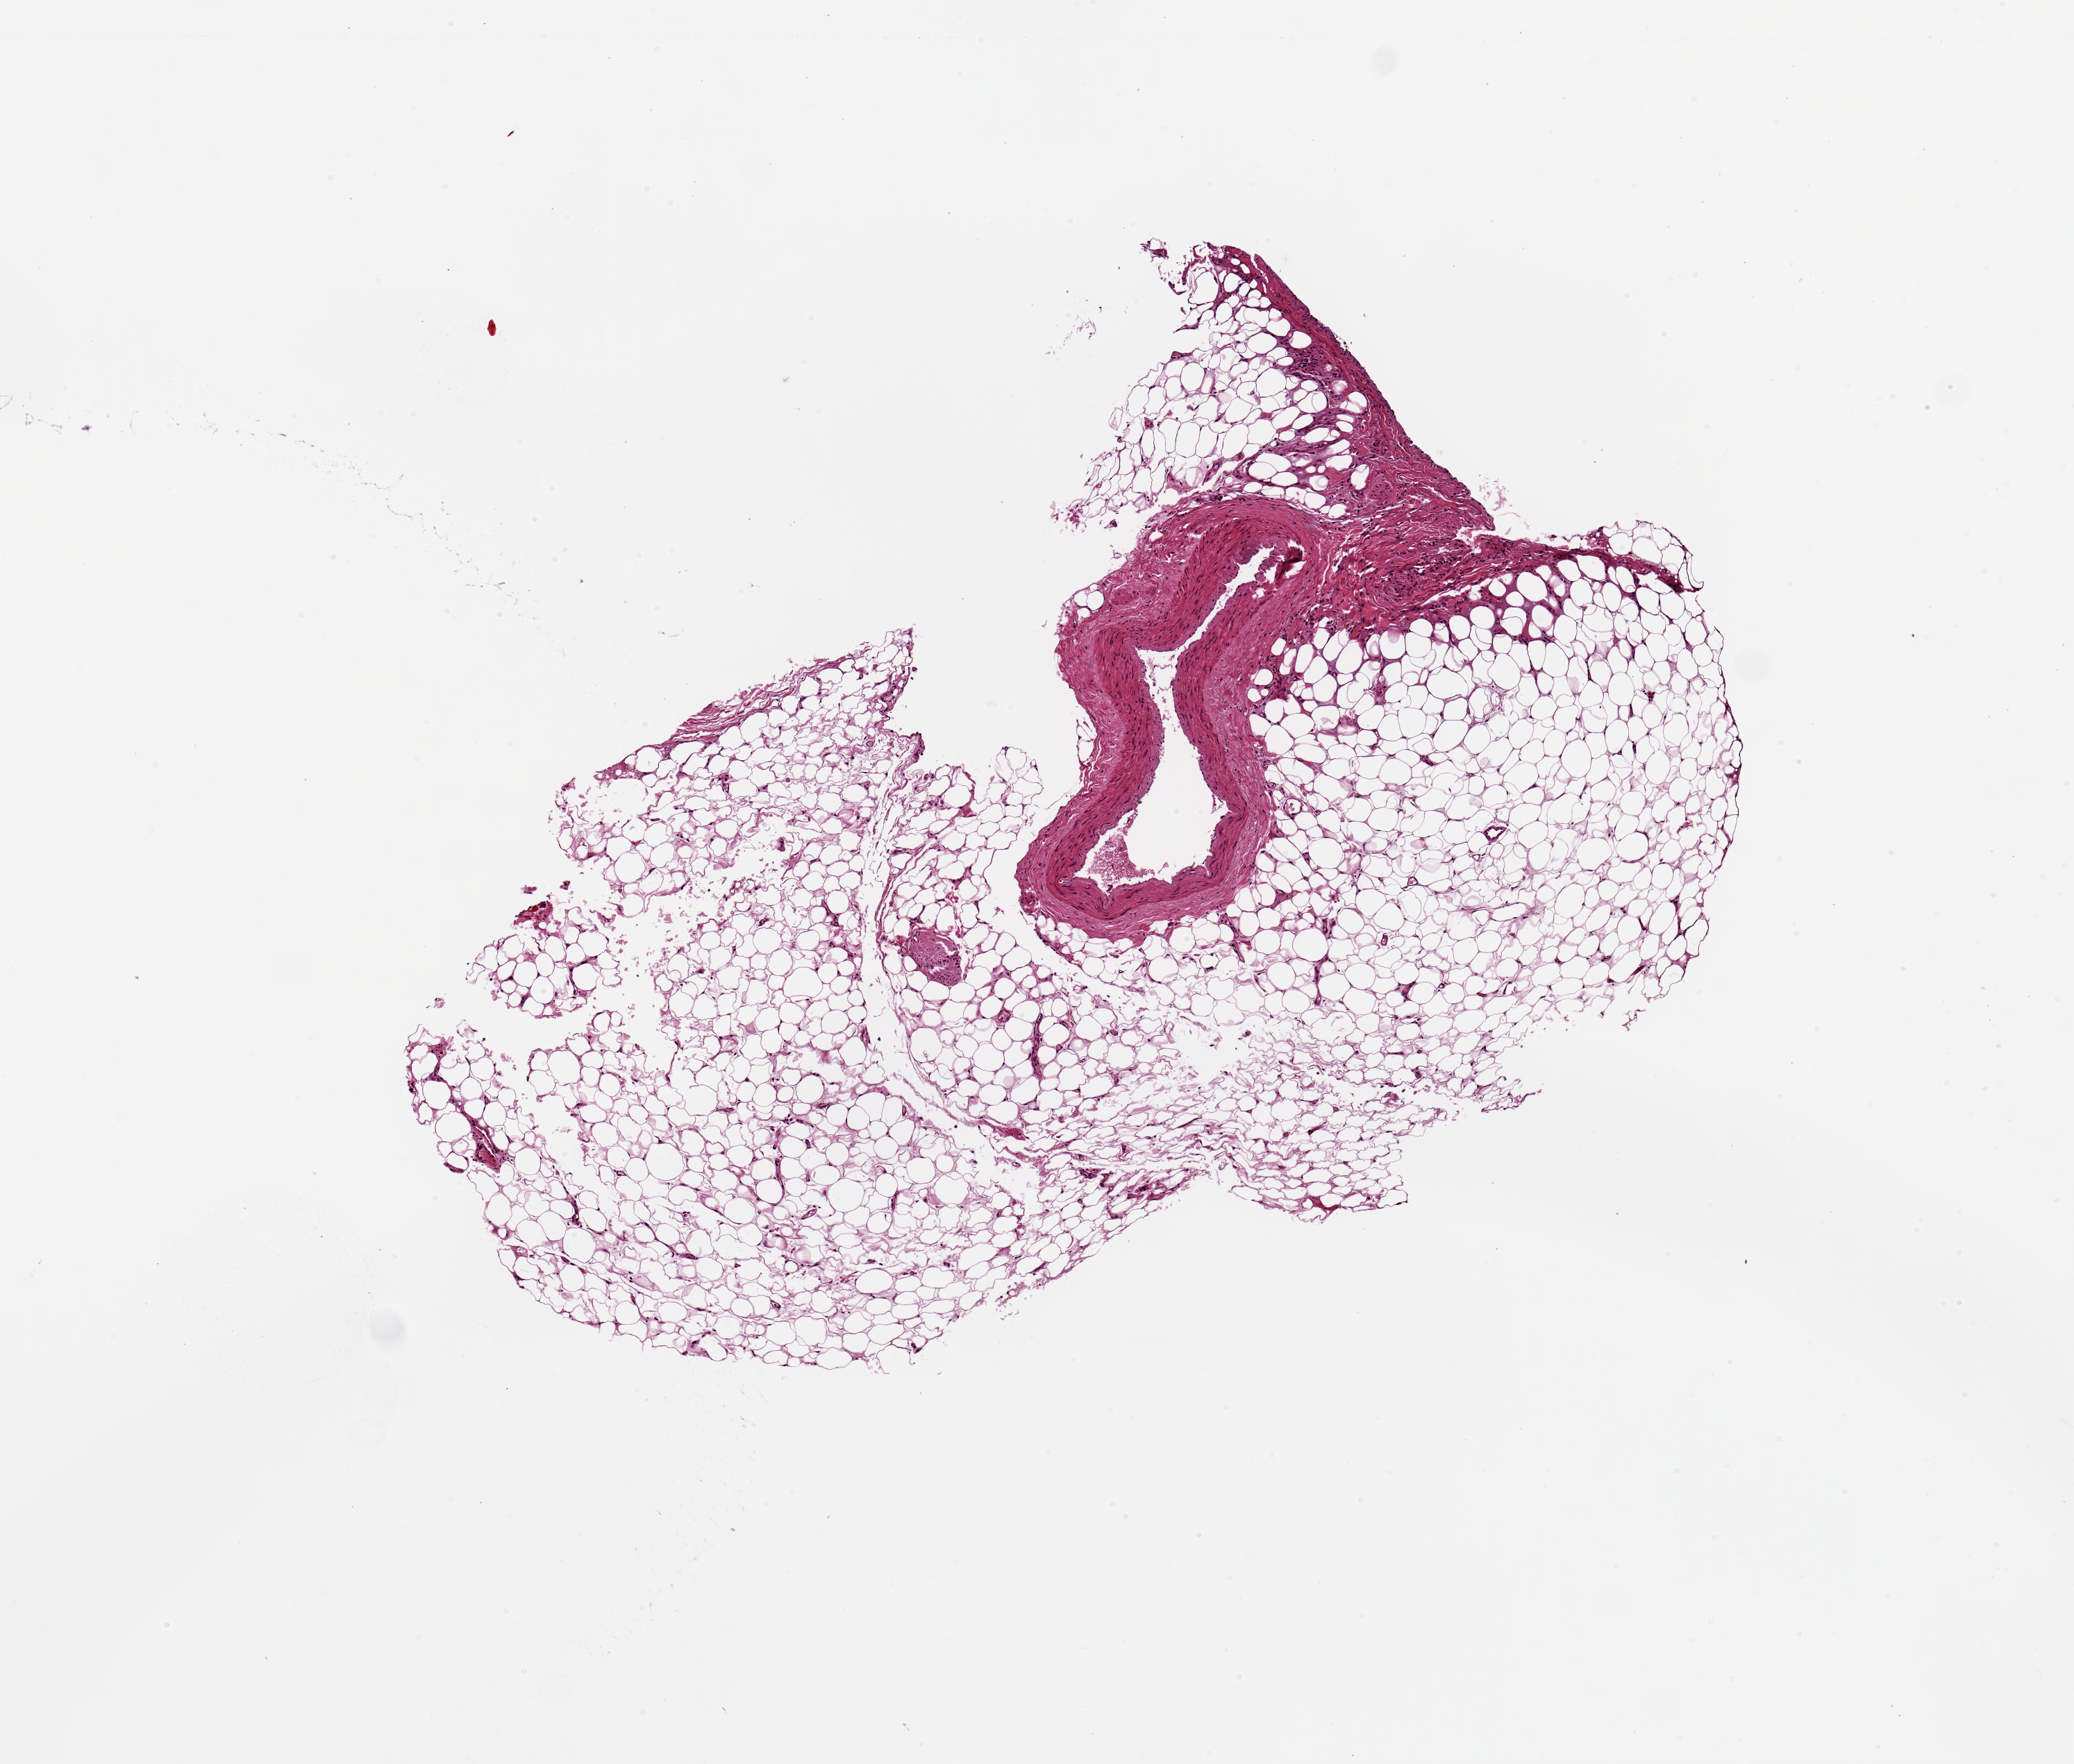
Digitized H&E-stained section — a low-resolution overview of the entire scanned area, about 5.9 x 5.0 mm; PAXgene-fixed paraffin-embedded (PFPE) section; target tissue: coronary artery; donor tissue sample. Donor sex: male.
Review note (as recorded): 4x1.8mmfat surrounds a 1 x0.2mm artery.